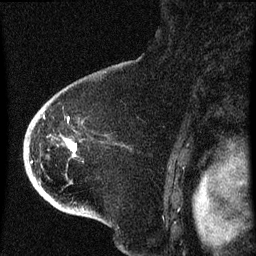
Breast MRI (dynamic contrast-enhanced), one sagittal slice. Position 48 of 60 along the scan axis. Dynamic contrast-enhanced series, image 2 of 4 at this slice position (ordered by acquisition). 1.5 T. TE 4.2 ms, TR 8 ms. 2 mm slice thickness. 256 × 256 image matrix, field of view 180 × 180 mm. Patient: female, 71 years.
Outlined on this slice (semi-automatically segmented with operator editing):
- analysis volume of interest (the breast-tissue region the enhancement analysis was run in; not a lesion): box from (x=32, y=86) to (x=89, y=205) px
- tumour enhancement mask (voxels above the 70 % enhancement threshold inside the analysis volume of interest): (x=43, y=116)–(x=77, y=153)